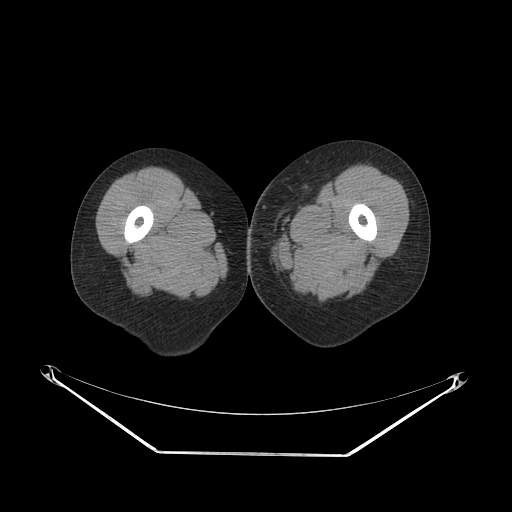
CT of an extremity soft-tissue mass (from a PET/CT study), one axial slice; reconstruction kernel SOFT; 140 kVp; soft-tissue window (W 400 / L 40 HU); 3.75 mm slice thickness; 512 × 512 image matrix. Female patient. Case-level facts recorded for this patient, not image findings: histological type: leiomyosarcoma; grade: high; site of the primary tumour: groin.
Outlined on this slice (expert contour drawn on MRI and transferred to this co-registered scan by the dataset authors):
- gross tumour volume including surrounding oedema: box from (x=247, y=215) to (x=277, y=248) px